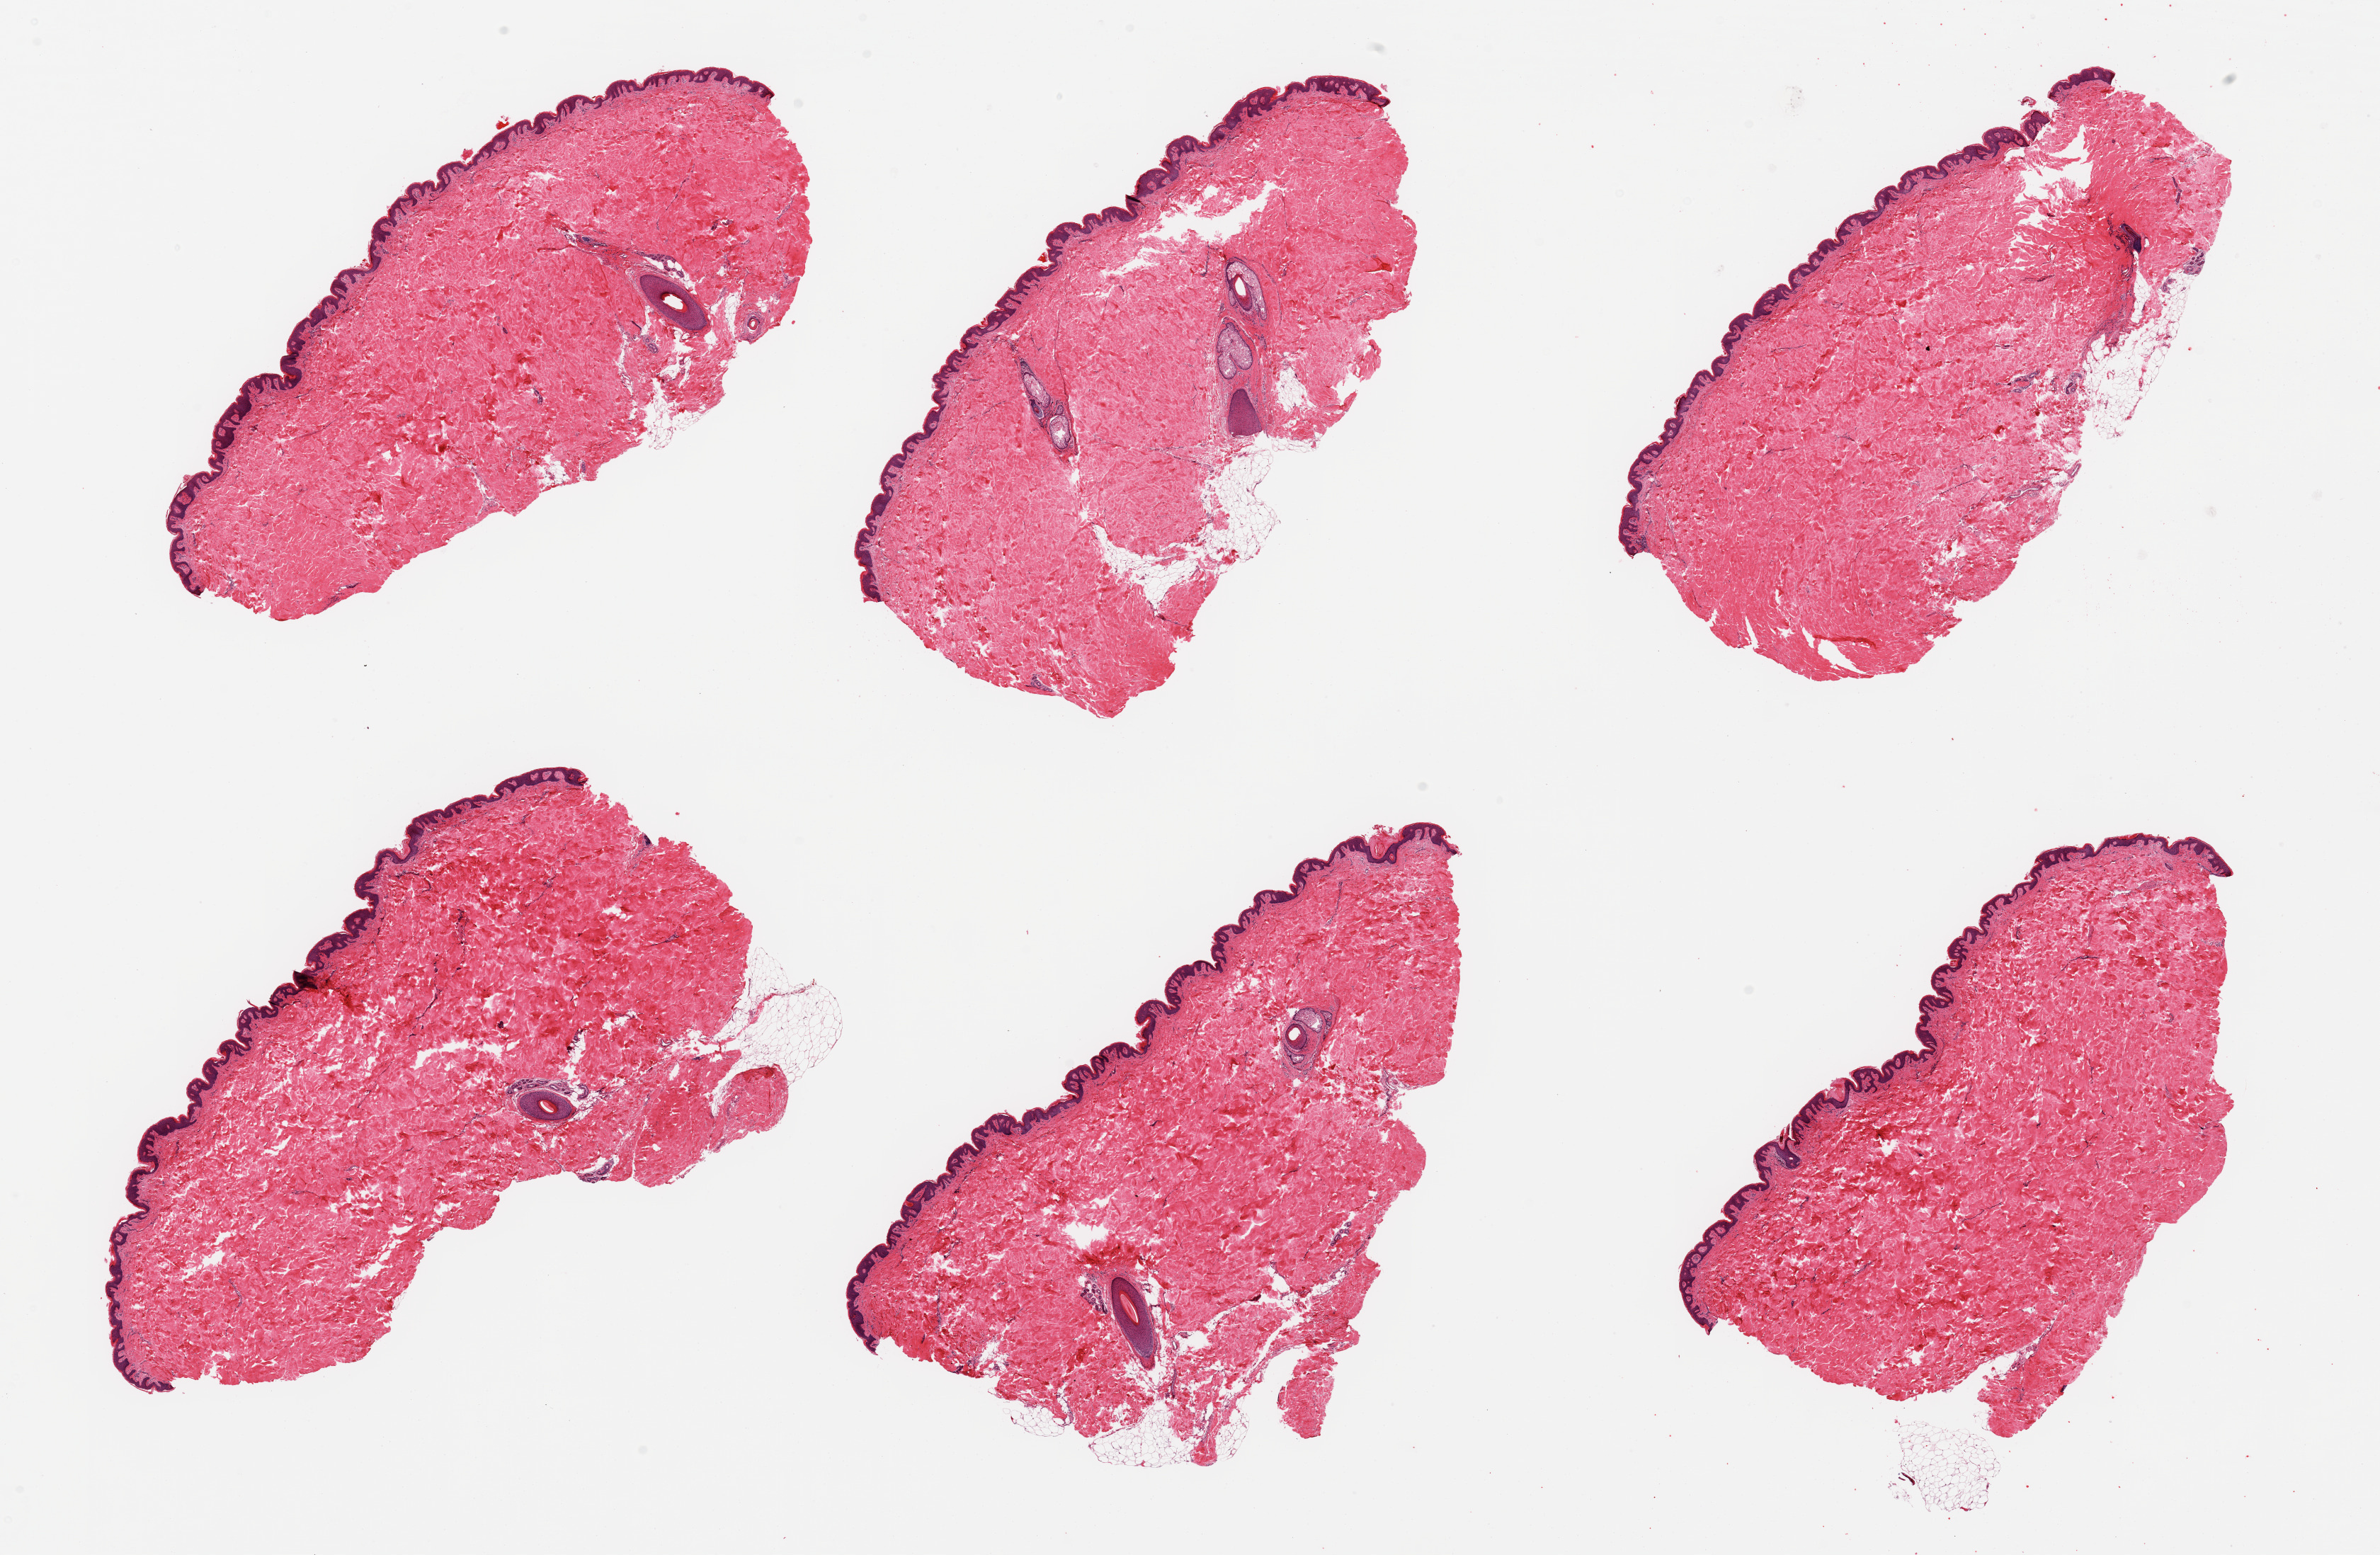
Digitized H&E-stained section, brightfield, a low-resolution overview of the entire scanned area, about 26.6 x 17.4 mm (from a 20x scan). PAXgene-fixed, paraffin-embedded tissue. Sampled site (target tissue): skin of suprapubic region. Donor tissue sample. Donor sex: male.
Review note (as recorded): 6 pieces; sparse internal/external fat; well trimmed.